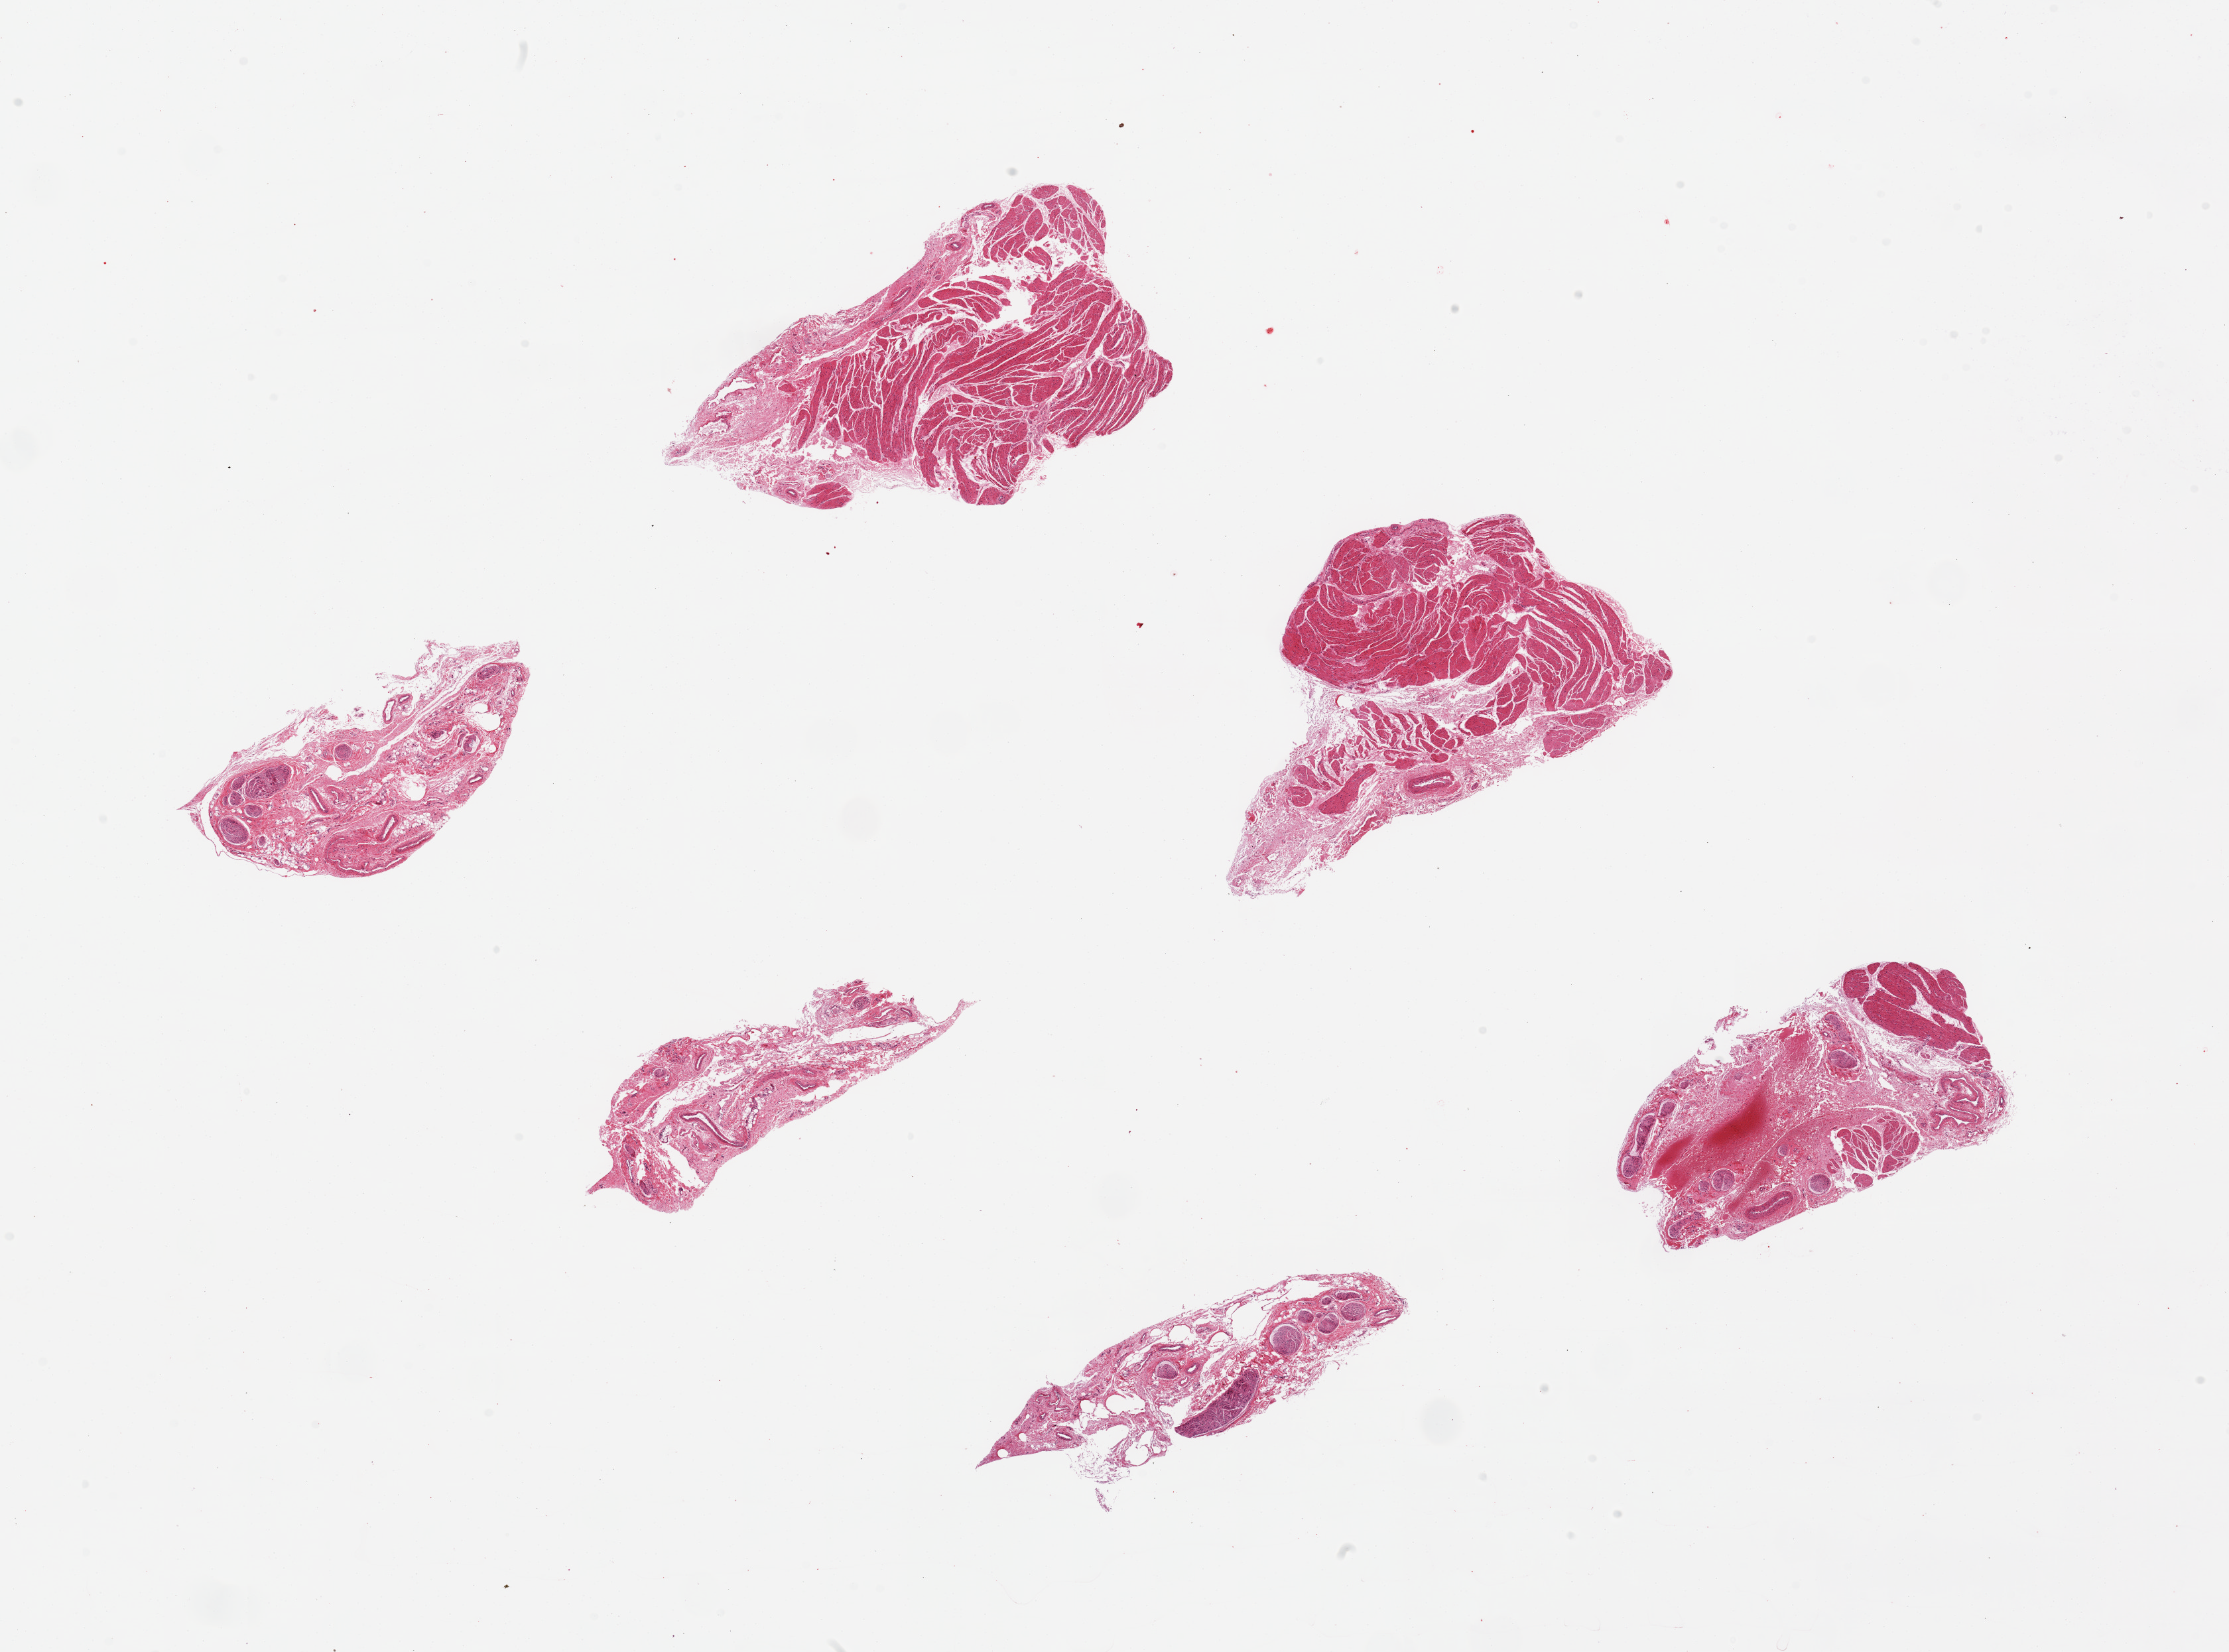
Digitized H&E-stained section — low-resolution overview of the scanned area, about 26.6 x 19.7 mm, PAXgene-fixed paraffin-embedded (PFPE) section, section of esophageal muscle (target tissue), tissue donor sample. Female donor.
Pathologist's review note for this sample: 6 pieces up to 6x3 mm;3 are muscularis 3 are adventitia.